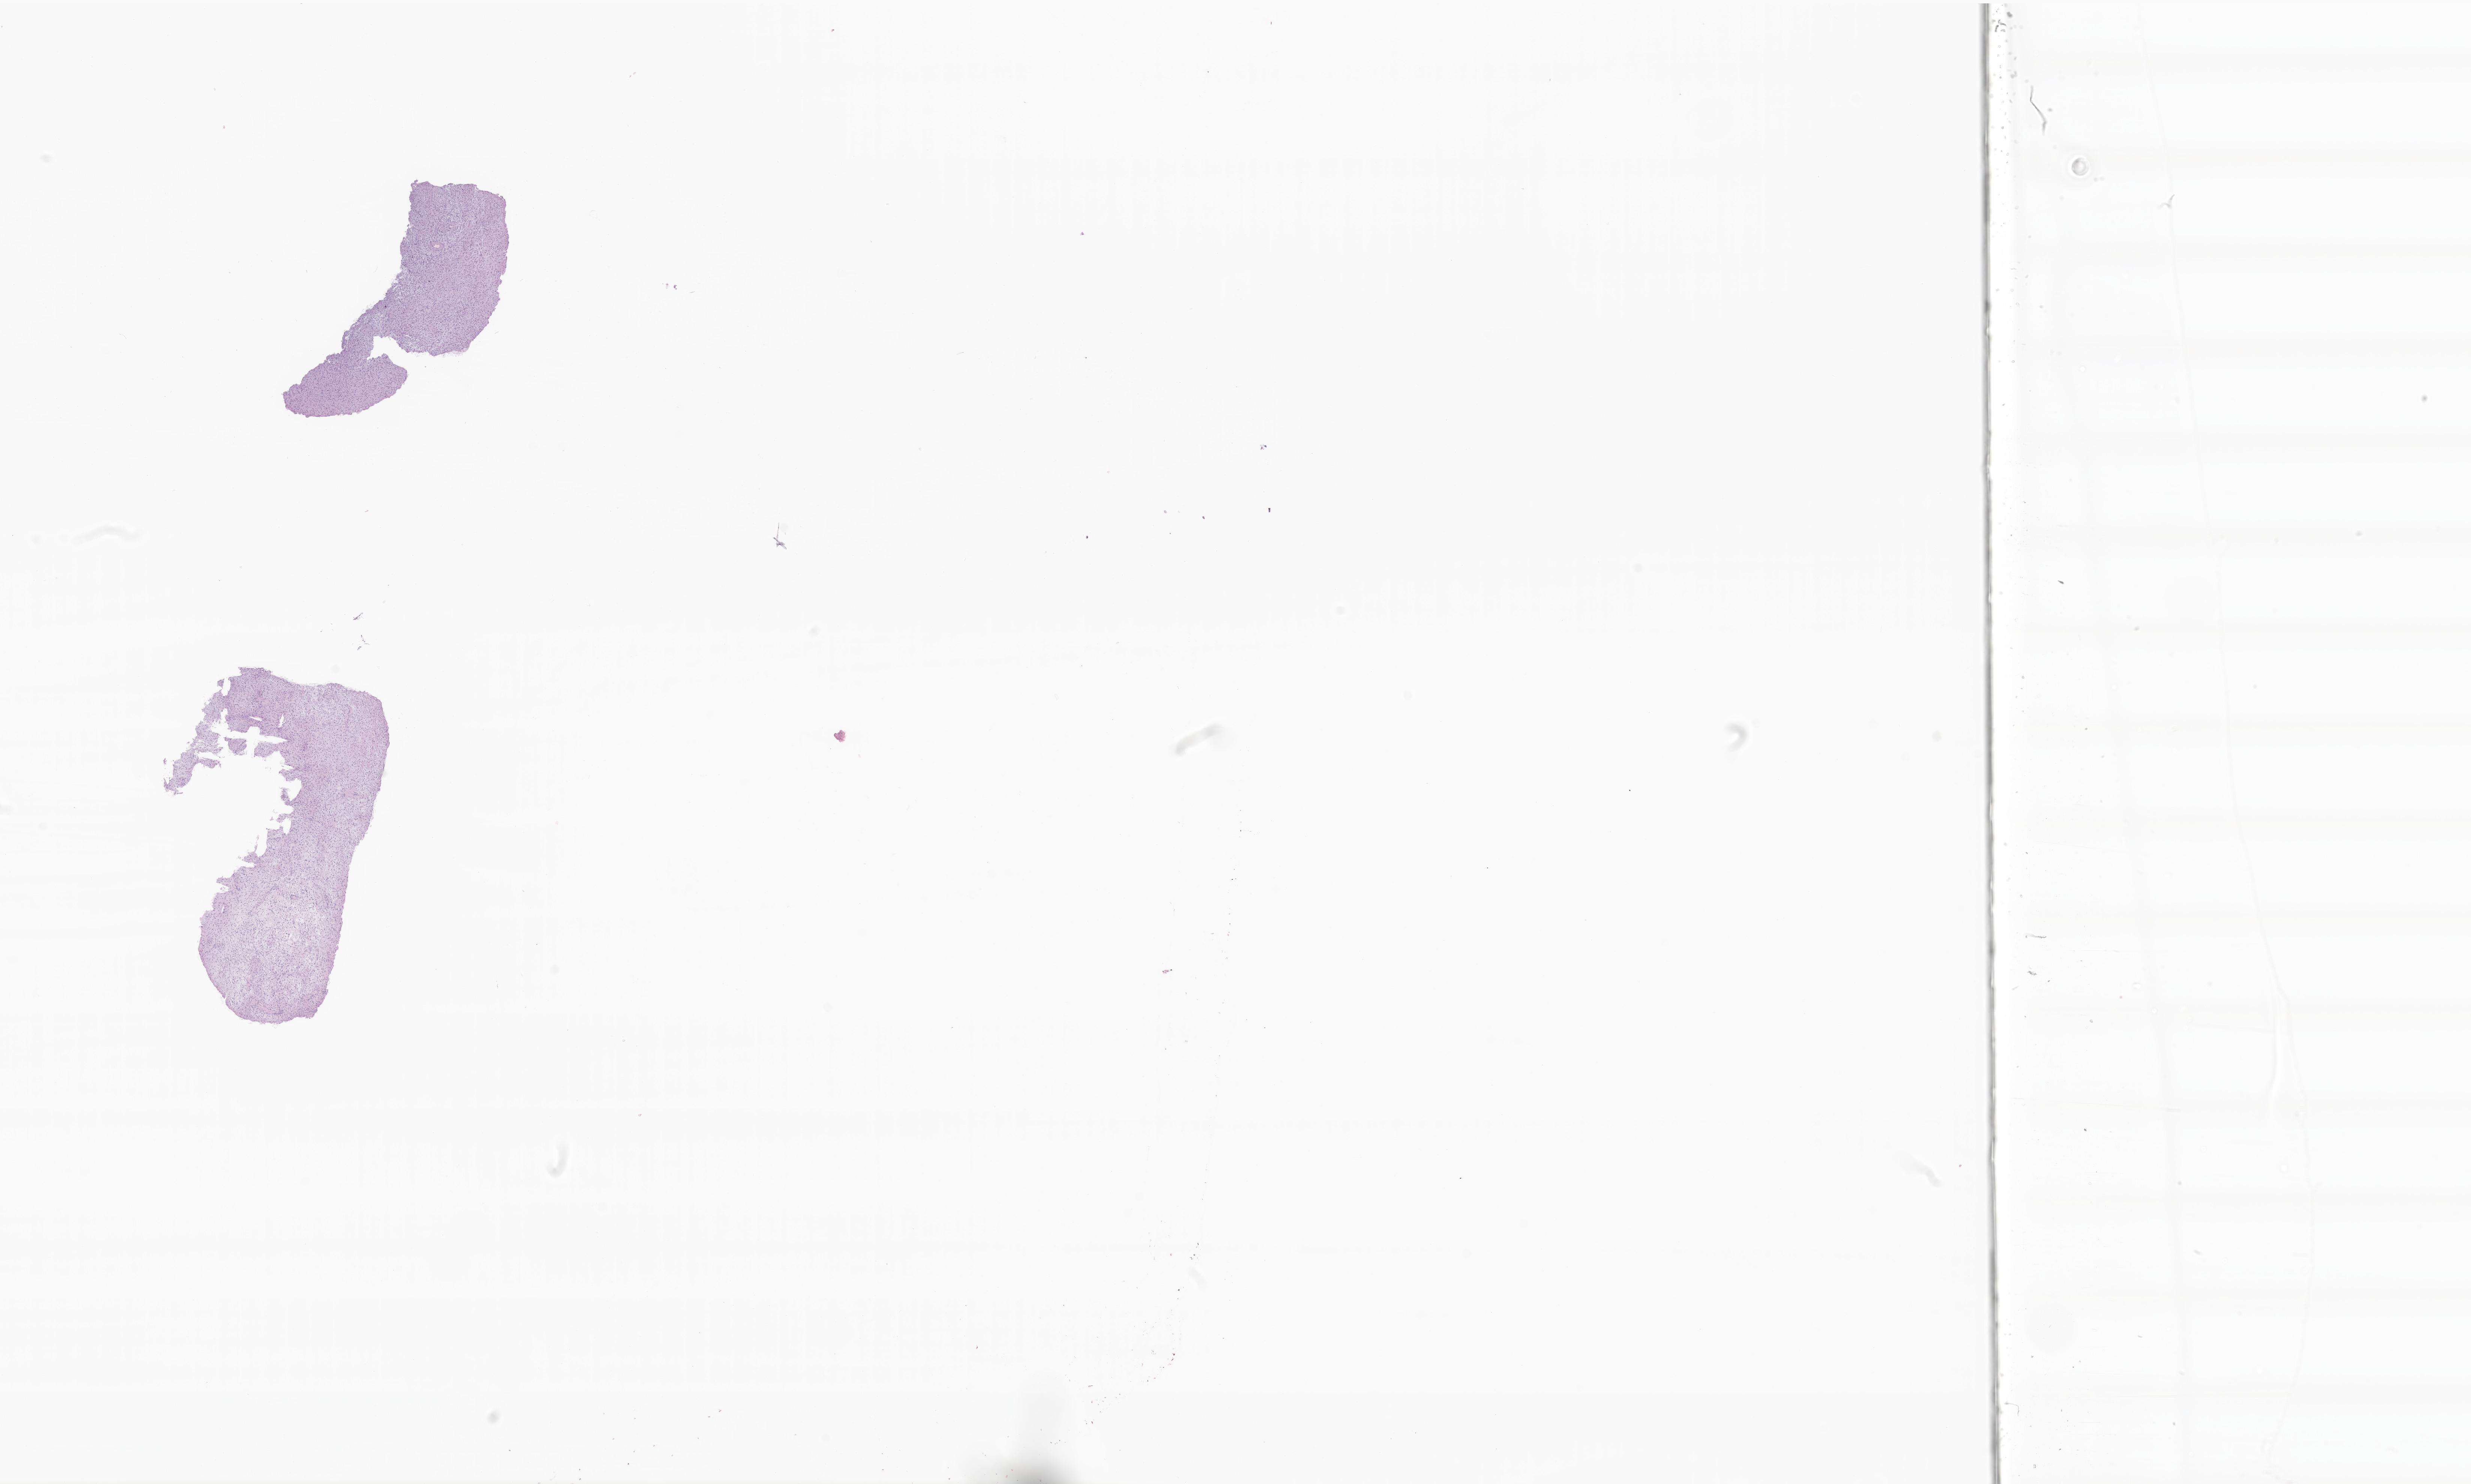
Whole-slide image, hematoxylin and eosin (H&E) stain of tumor tissue from the brain, whole scanned area (about 27.8 x 16.7 mm) shown as a low-resolution overview; formalin-fixed, paraffin-embedded (FFPE) tissue. Female patient, age 161 months (13 years 5 months).
Diagnosis: Pilocytic astrocytoma.